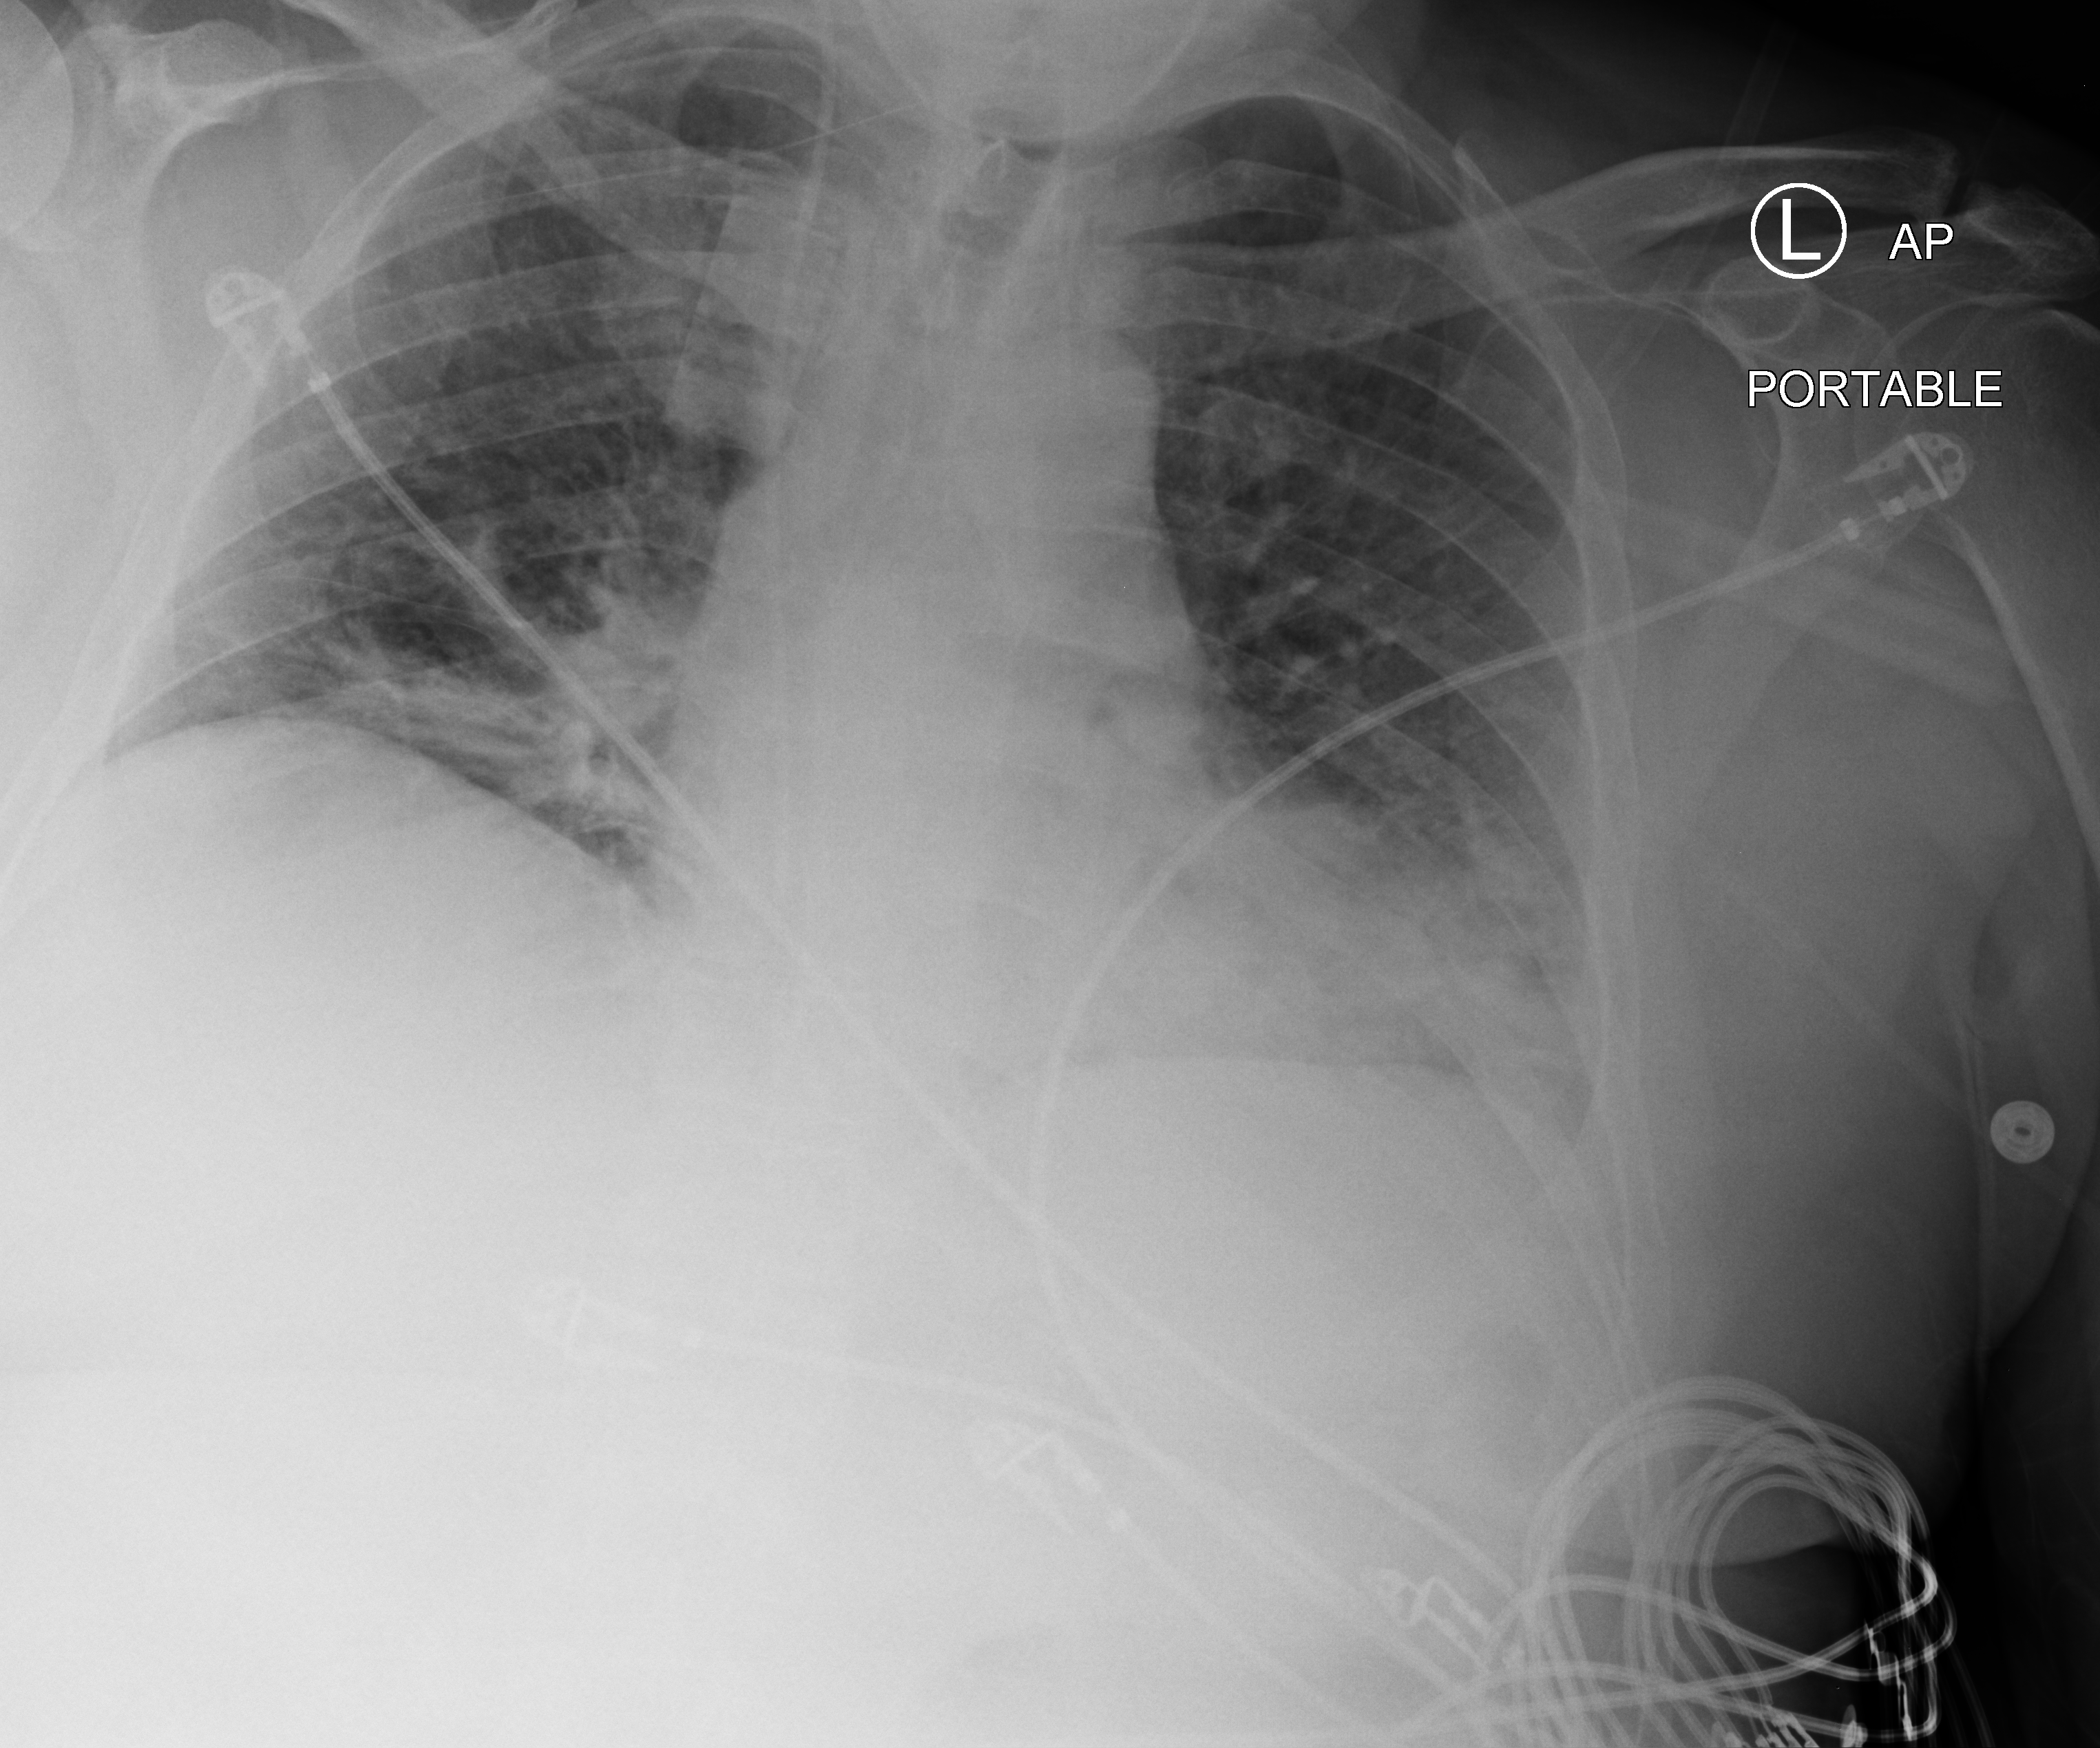
Portable chest radiograph; anteroposterior (AP) projection. Patient hospitalised with COVID-19; male, aged 18–59 years.
Admission-level facts for this patient (not findings on this image; timing relative to this image not recorded):
- admitted to intensive care during this hospital stay: yes
- length of hospital stay: 17 days
- smoking status (admission record): never